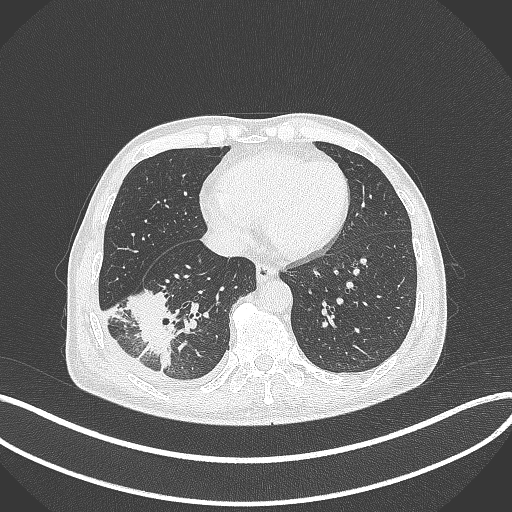
Chest CT, one axial slice. Position 122 of 388 along the scan axis. Lung window (W 1500 / L -600 HU). 512 × 512 image matrix. Patient: male, 64 years. From the clinical record (not read from this slice): clinical TNM (as recorded): T3 N0 M0; histopathological grade: G2-3.
Structures marked on this image (bounding box drawn by a radiologist):
- lung tumour (recorded histology: adenocarcinoma): bounding box (x1, y1, x2, y2) in pixels: (116, 282, 177, 373)